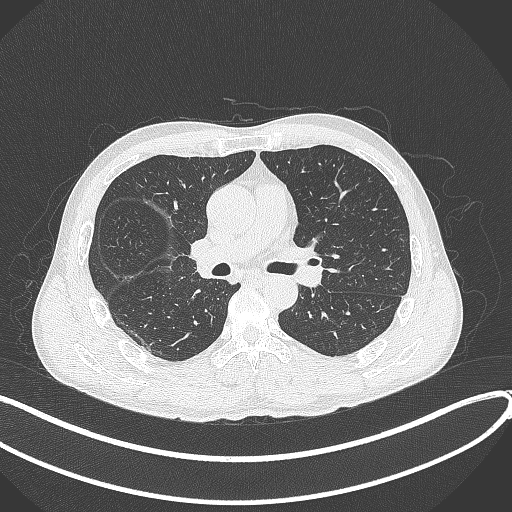
Chest CT, one axial slice. Slice 223 of 409 in the series (ordered by position). 120 kVp. Lung window (W 1500 / L -600 HU). 1 mm slice thickness. 512 × 512 image matrix, field of view 400 × 400 mm. Male patient, age 53 years. Case-level facts recorded for this patient, not image findings: clinical TNM (as recorded): T1b N0 M0.
Structures marked on this image (rectangle marked by the reading radiologist):
- lung tumour (recorded histology: squamous cell carcinoma): box from (x=187, y=236) to (x=222, y=273) px